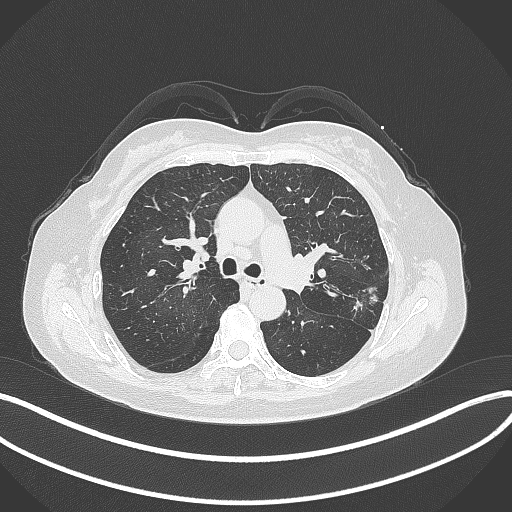
Chest CT, one axial slice. Position 205 of 319 along the scan axis. Reconstruction kernel B70f. 120 kVp. Lung window (W 1500 / L -600 HU). 1 mm slice thickness. 512 × 512 image matrix, field of view 400 × 400 mm. Female patient, age 60 years. From the clinical record (not read from this slice): clinical TNM (as recorded): T1c N0 M0.
Outlined on this slice (rectangle marked by the reading radiologist):
- lung tumour (recorded histology: adenocarcinoma): bounding box [x1, y1, x2, y2] px = [349, 283, 380, 314]